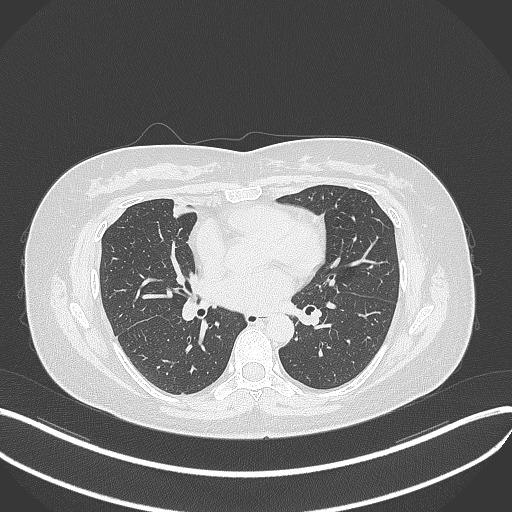
Chest CT, one axial slice. Position 152 of 273 along the scan axis. 120 kVp. Lung window (W 1500 / L -600 HU). 1 mm slice thickness. 512 × 512 image matrix. Patient: female, 42 years. Case-level facts recorded for this patient, not image findings: clinical TNM (as recorded): T1b N0 M0.
Outlined on this slice (rectangle marked by the reading radiologist):
- lung tumour (recorded histology: adenocarcinoma): bounding box [x1, y1, x2, y2] px = [170, 198, 200, 221]